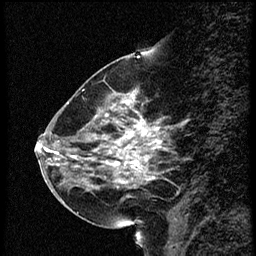
Breast MRI (dynamic contrast-enhanced), one sagittal slice; dynamic contrast-enhanced study with each time point stored as its own series, time point 2 of 4 at this slice position (early post-contrast, ordered by acquisition time); 1.5 T; TE 4.2 ms, TR 18.9 ms; 2 mm slice thickness; 256 × 256 image matrix, field of view 200 × 200 mm. Female patient. From the clinical record (not read from this slice): setting: breast cancer imaged before/during neoadjuvant chemotherapy; receptor status: HER2-positive.
Outlined on this slice (semi-automatic segmentation, software-assisted and operator-edited):
- analysis volume of interest (the breast-tissue region the enhancement analysis was run in; not a lesion): bounding box <63,80,168,215> (left, top, right, bottom; pixels)
- tumour enhancement mask (voxels above the 100 % enhancement threshold inside the analysis volume of interest): <96,94,161,183>